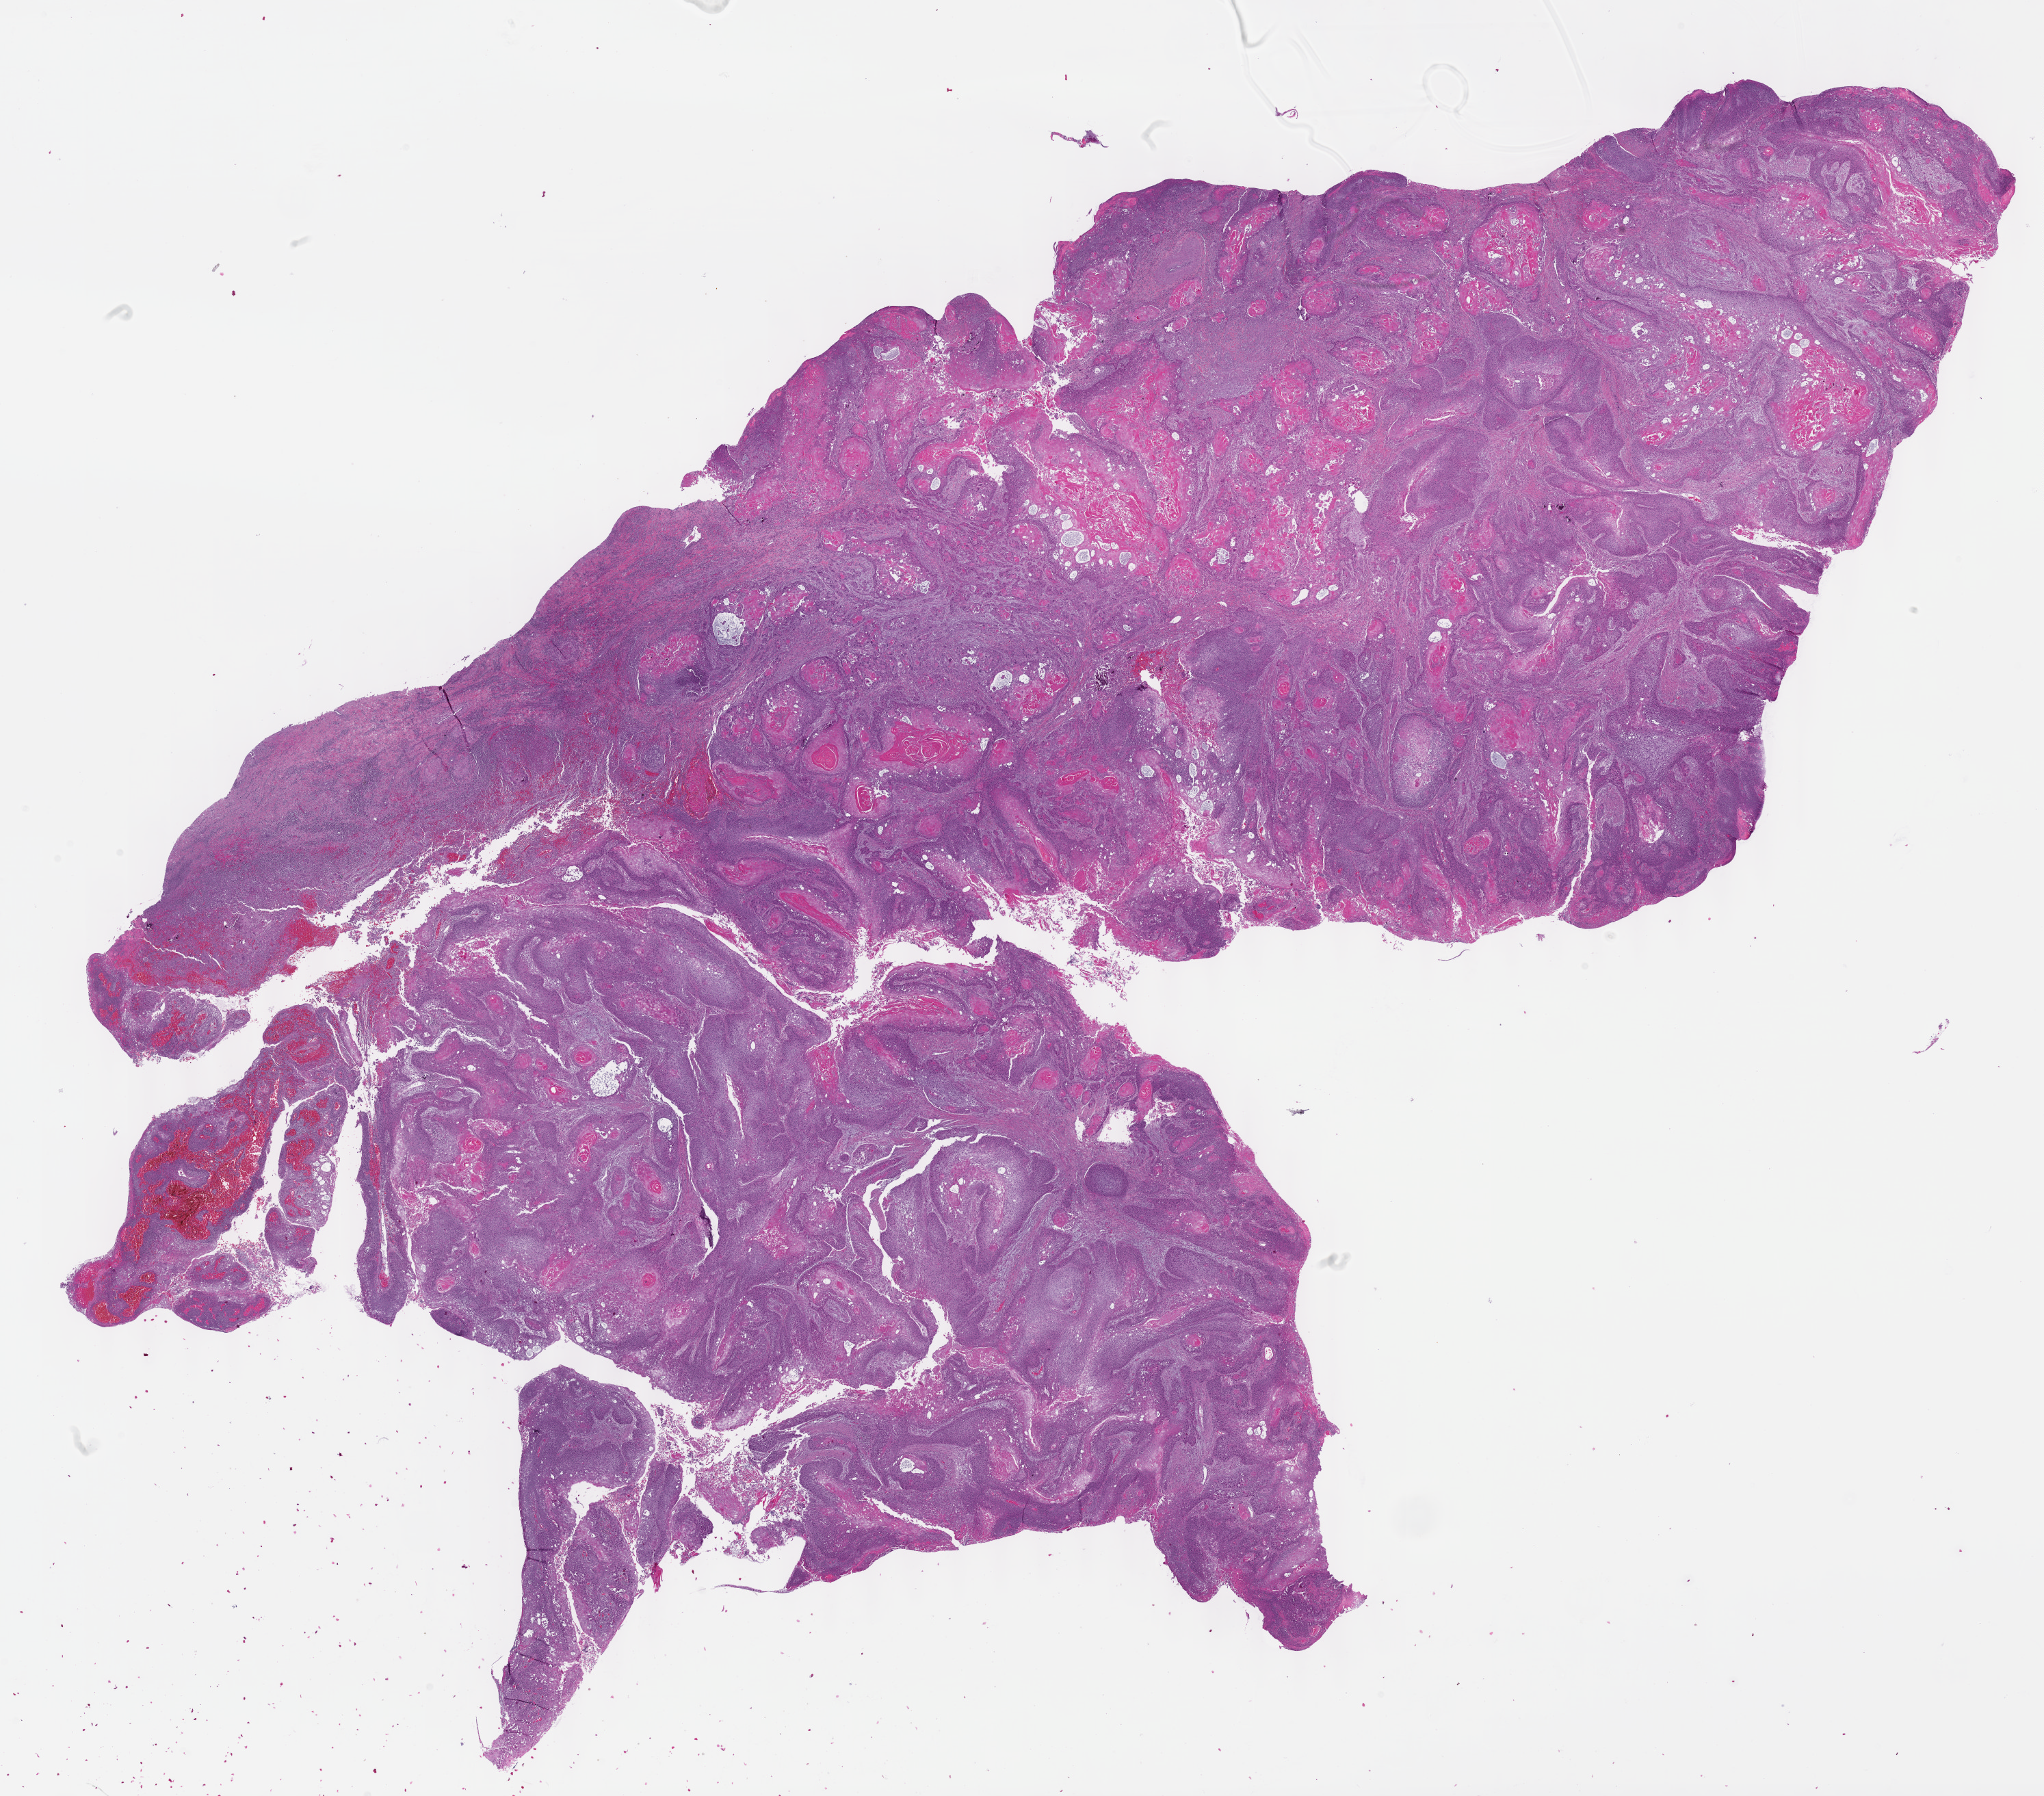
Whole-slide histology image, Hematoxylin and eosin (H&E) stained, shown as a low-resolution overview of the whole scanned area (about 24.1 x 21.2 mm, from a 40x scan); FFPE section; primary tumour sample from the head and neck. Male patient; age at initial diagnosis 62 years. Histologic grade: G2 (moderately differentiated).
AJCC pathologic stage: IVA. Diagnosis: Squamous cell carcinoma, NOS (larynx, NOS).